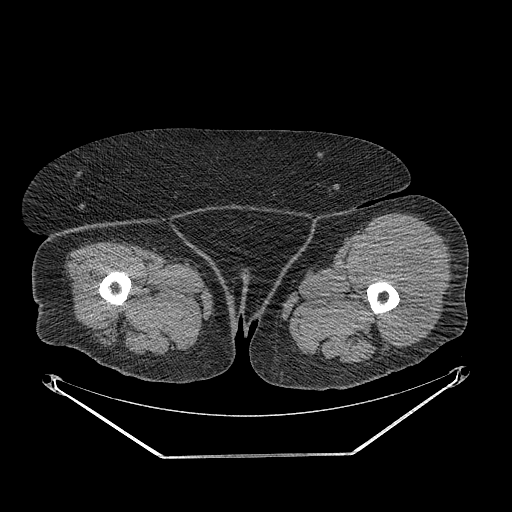
CT of an extremity soft-tissue mass (from a PET/CT study), one axial slice; reconstruction kernel STANDARD; 140 kVp; soft-tissue window (W 400 / L 40 HU); 3.75 mm slice thickness; 512 × 512 image matrix, field of view 500 × 500 mm. Female patient. Case-level facts recorded for this patient, not image findings: histological type: undifferentiated – high grade; grade: high; site of the primary tumour: left thigh.
Structures marked on this image (expert contour drawn on MRI and transferred to this co-registered scan by the dataset authors):
- gross tumour volume including surrounding oedema: bounding box [x1, y1, x2, y2] px = [356, 237, 435, 348]
- gross tumour volume (mass): [358, 244, 433, 344]